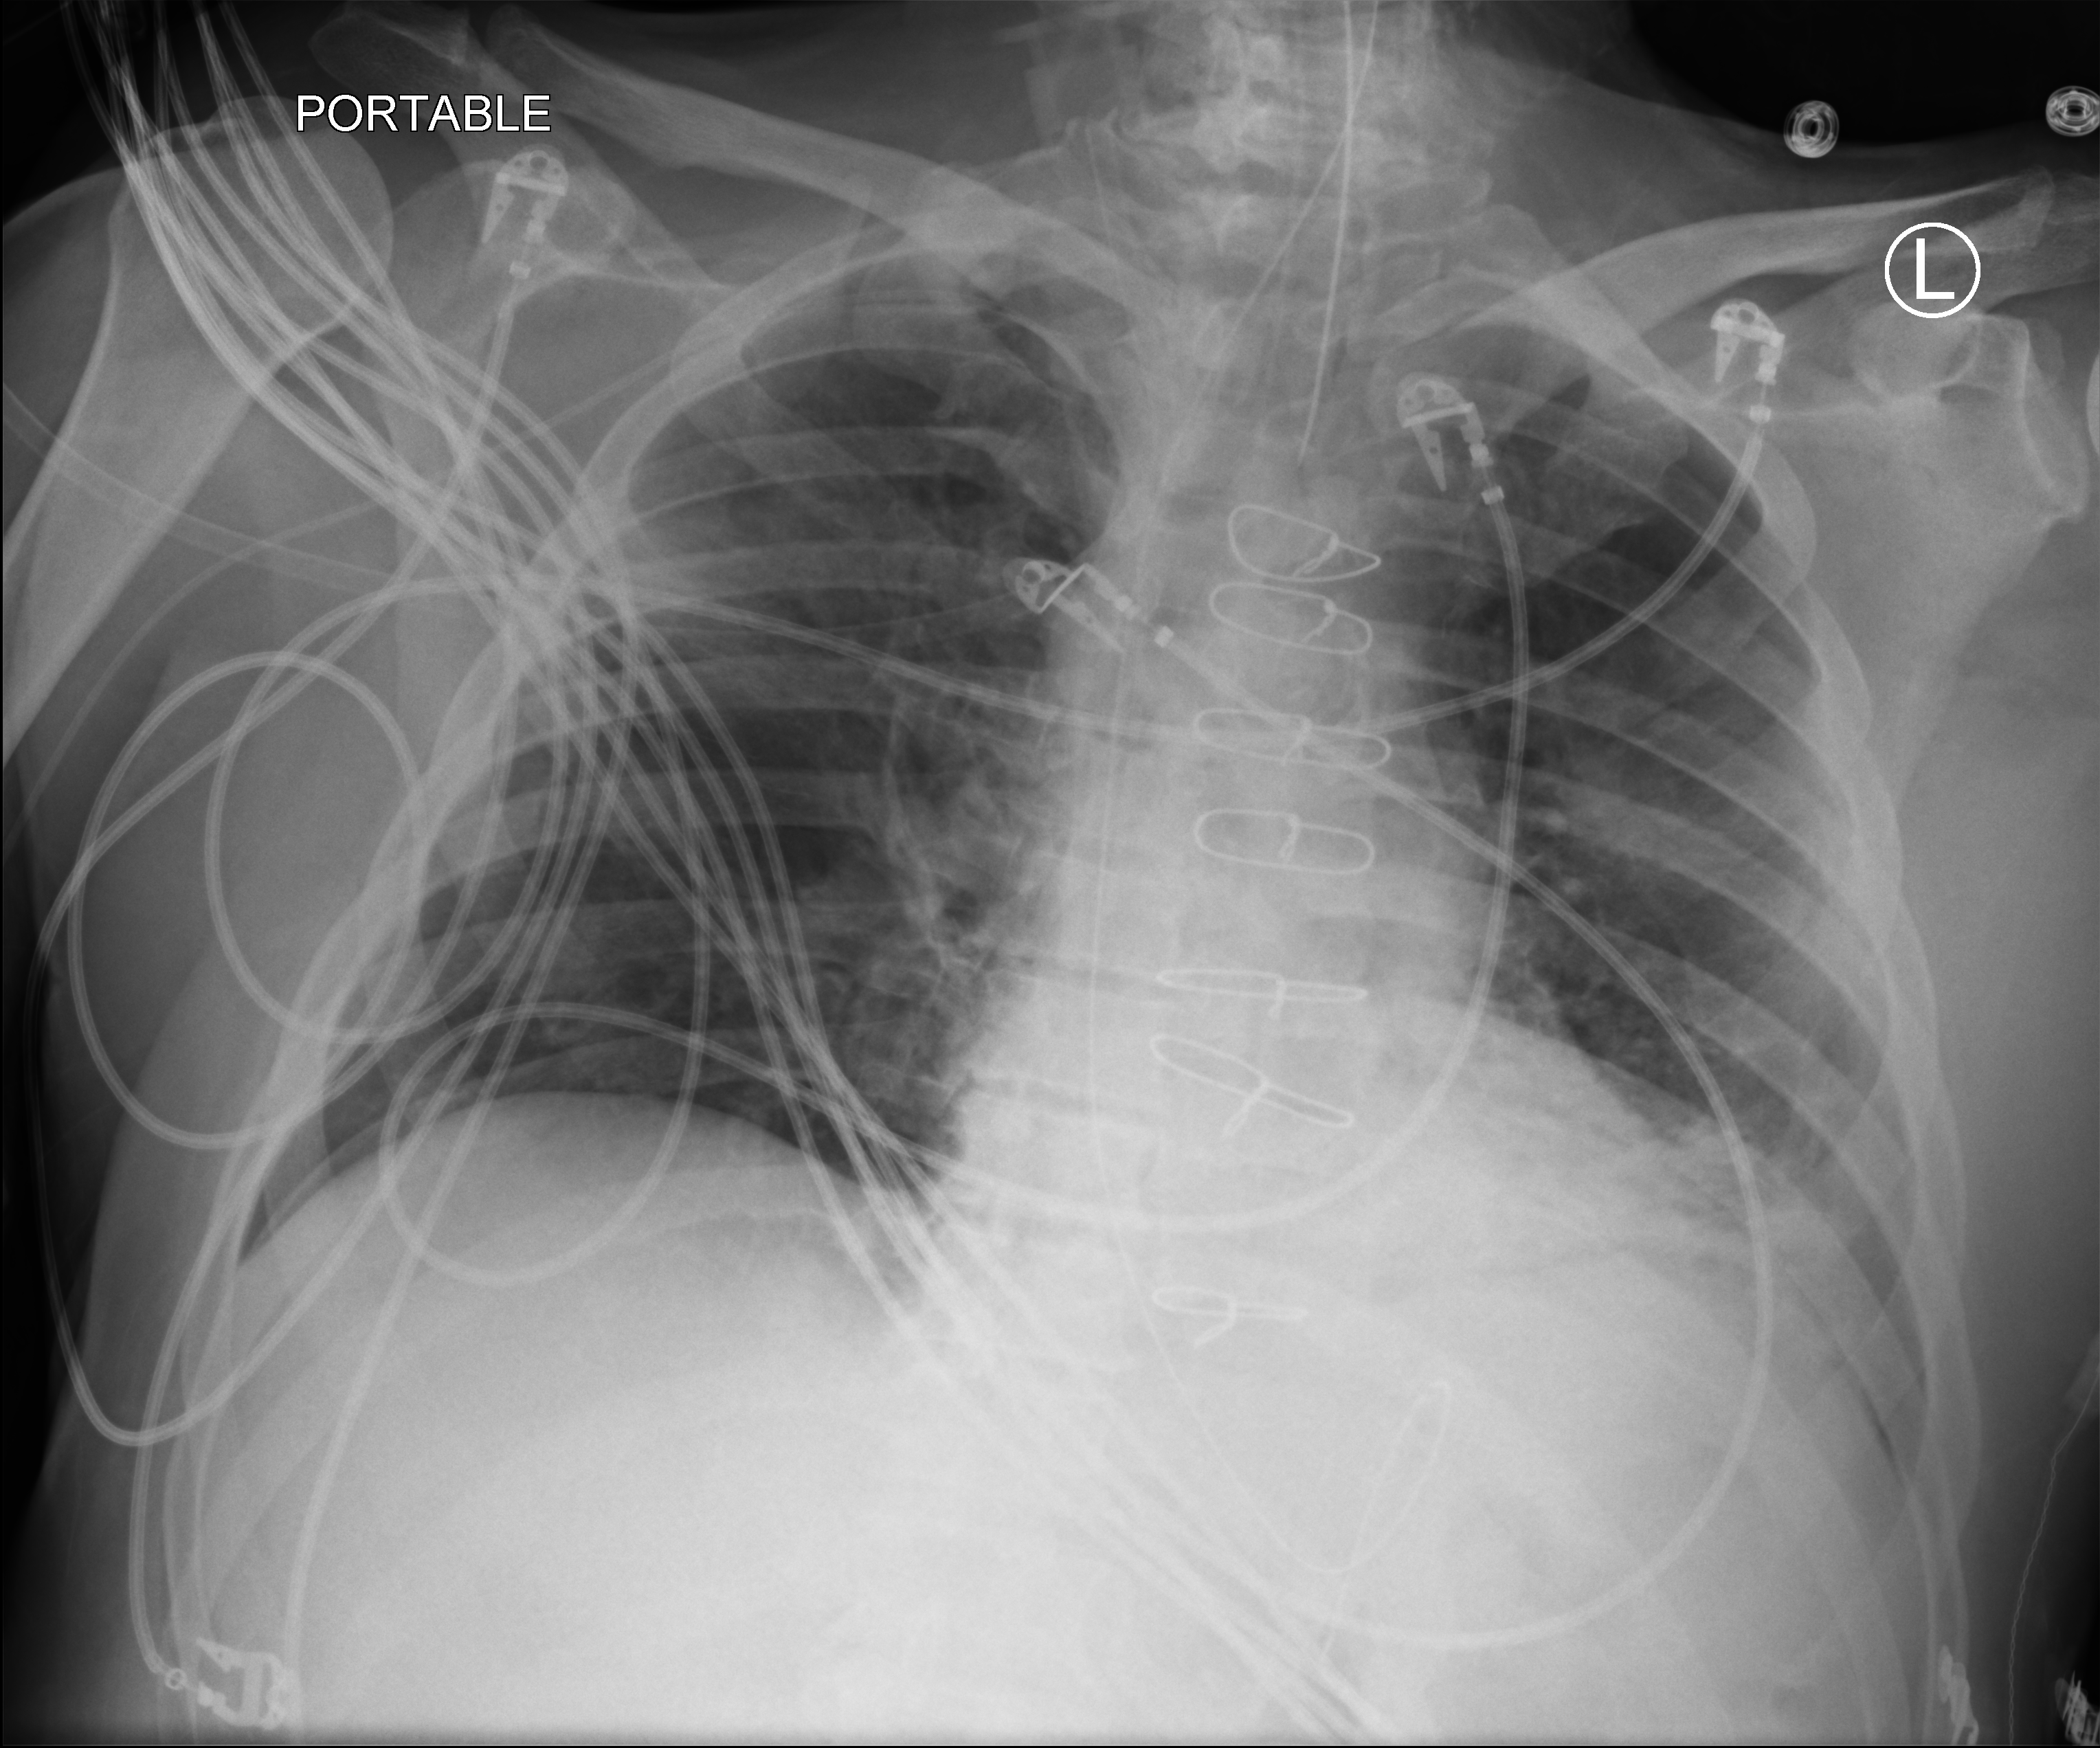
Chest X-ray (portable); anteroposterior (AP) projection. Male patient hospitalised with COVID-19, age 60–74 years.
From the hospital-stay record, not from the radiograph (when in the stay this image was taken is not recorded): chronic kidney disease (admission record): no; mechanically ventilated during this hospital stay: yes.